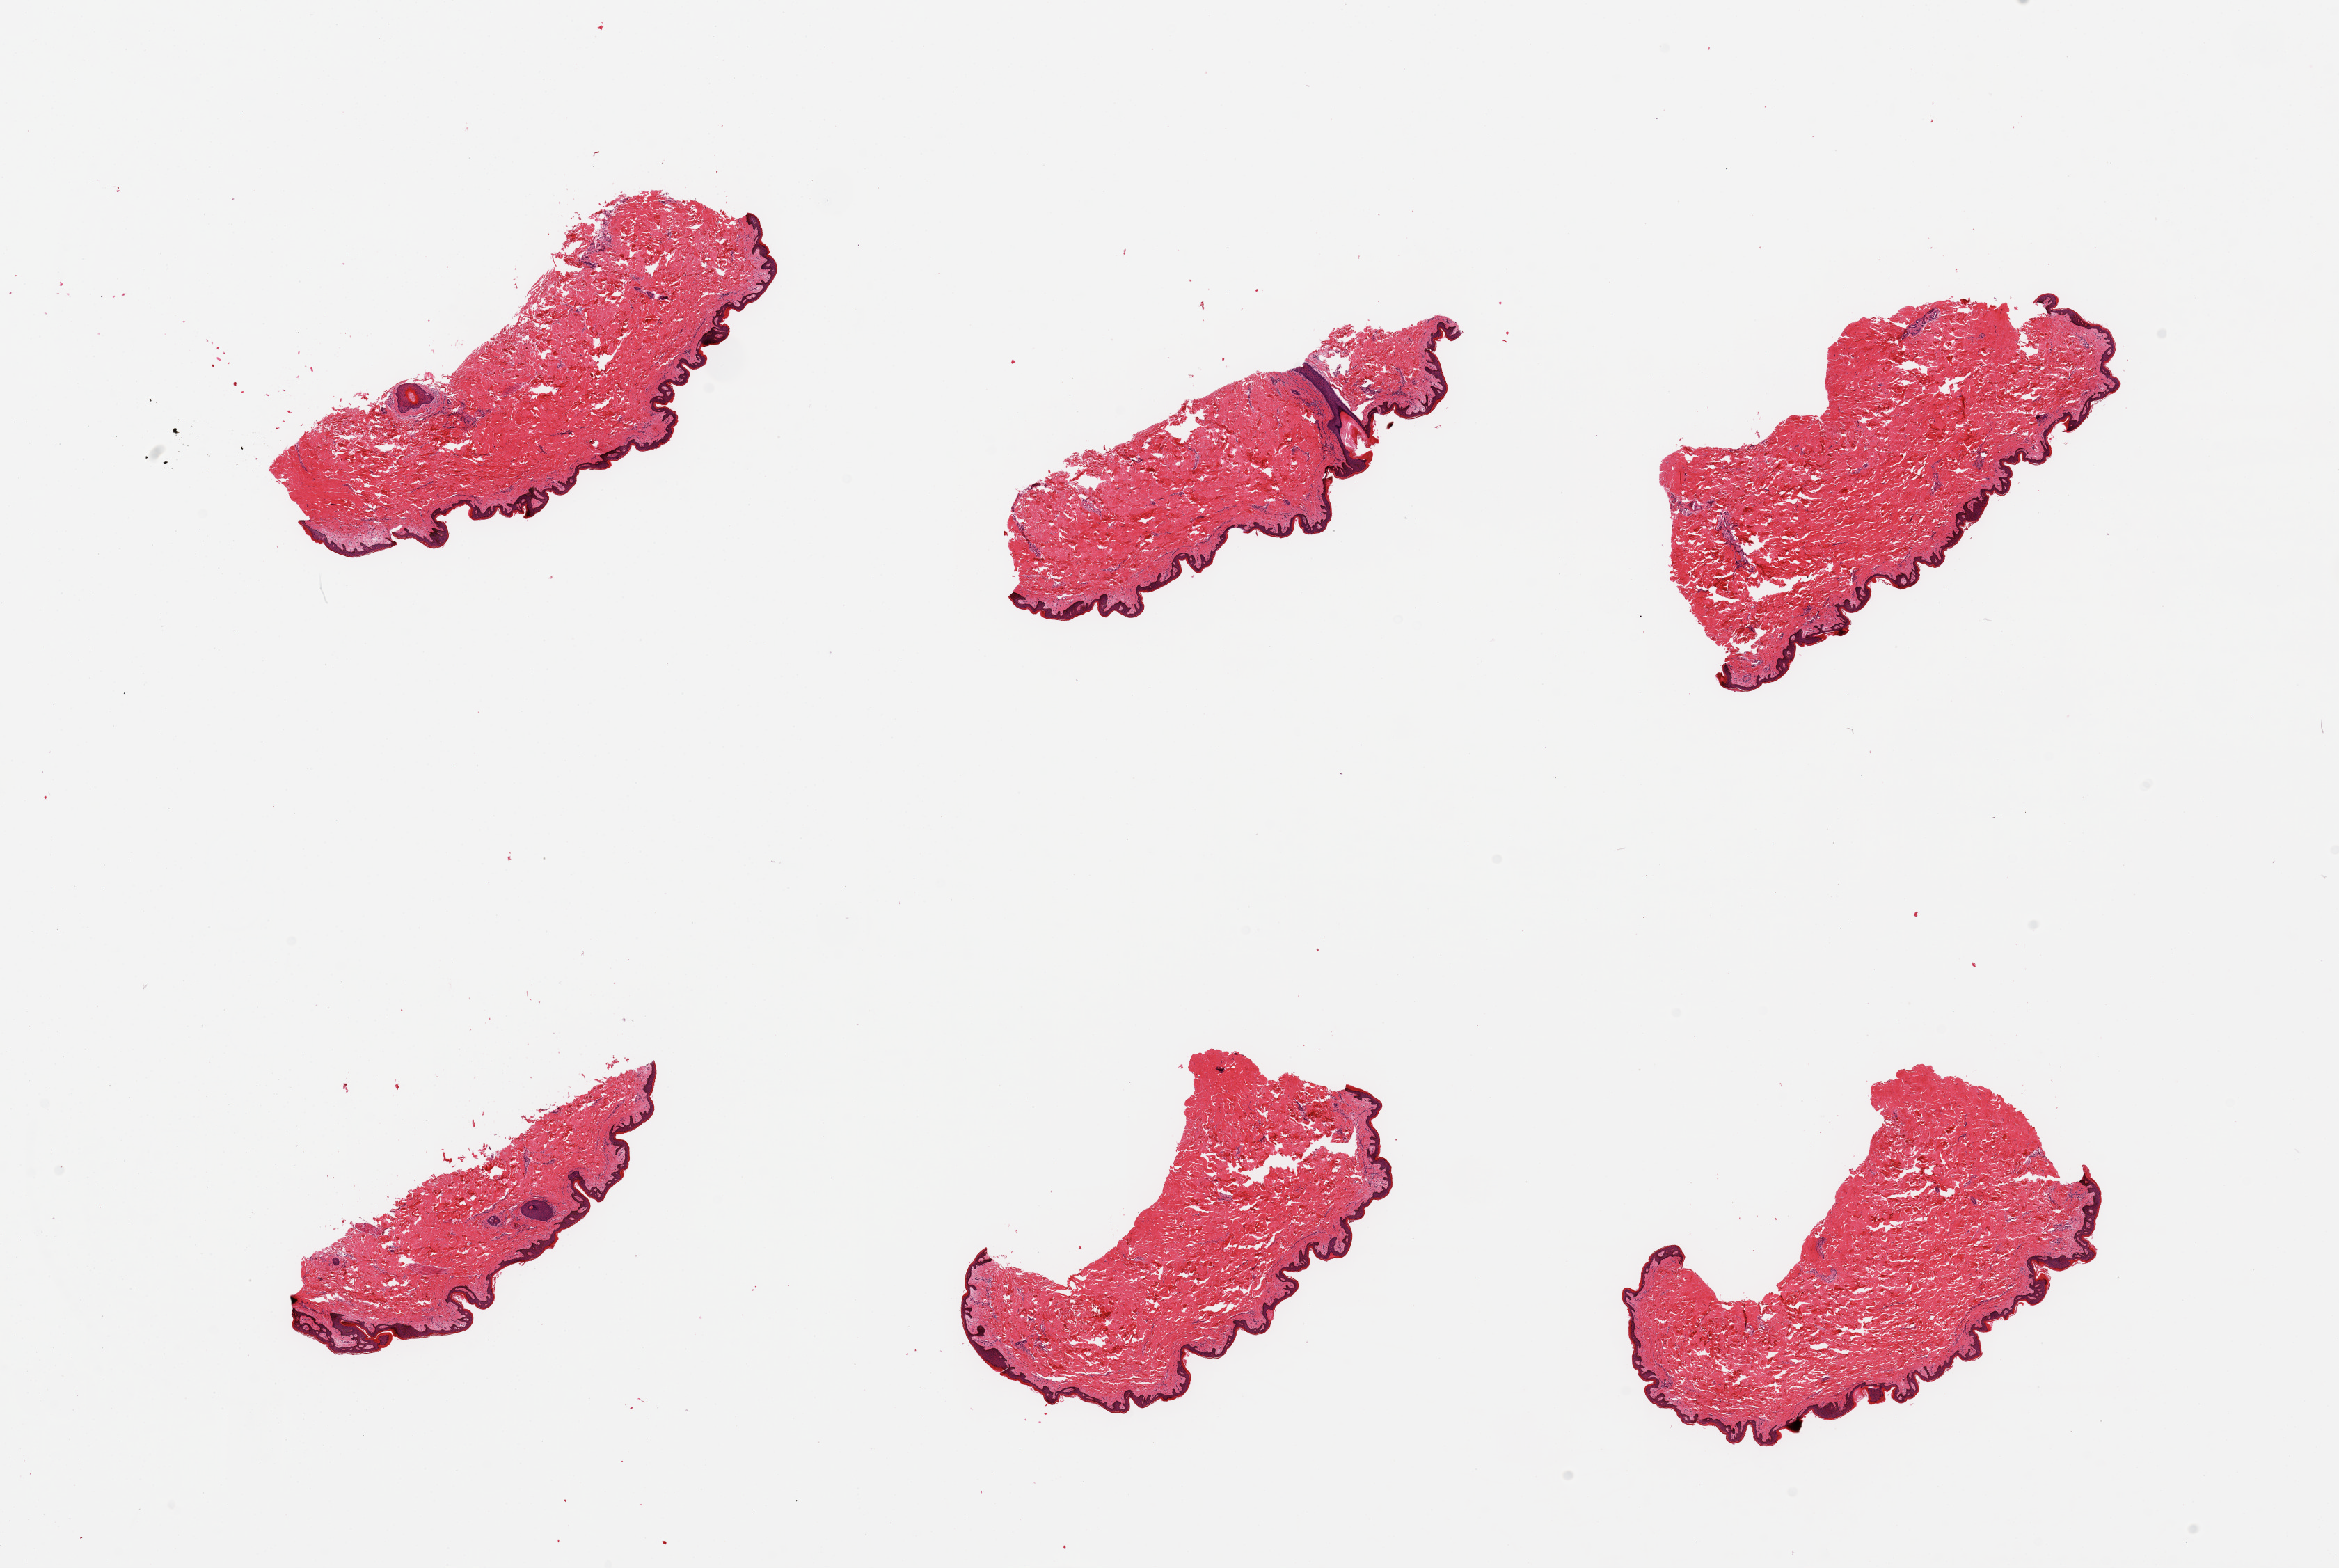
Whole-slide image, hematoxylin and eosin (H&E) stain, a low-resolution overview of the entire scanned area, about 26.6 x 17.8 mm (slide scanned at 20x), PAXgene-fixed, paraffin-embedded tissue, target tissue: skin of suprapubic region, donor tissue sample.
Reviewer comment on this tissue sample: 6 pieces; well trimmed, no intradermal fat.